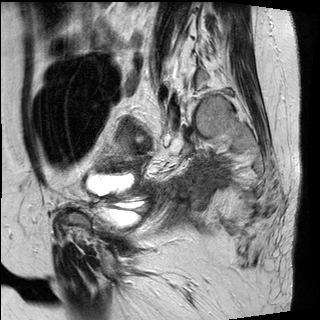
Pelvic MRI for cervical cancer, one sagittal slice; position 9 of 30 along the scan axis; T2-weighted; 1.5 T; TE 89 ms, TR 2930 ms; 4 mm slice thickness; 320 × 320 image matrix, field of view 260 × 260 mm. Patient: female, 62 years.
Annotated regions visible in this slice (expert manual segmentation):
- uterus and cervix: bounding box [x1, y1, x2, y2] px = [114, 120, 134, 144]